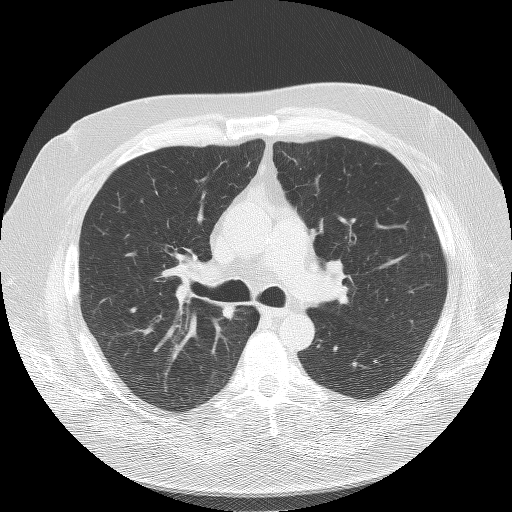
Axial slice from a low-dose chest CT screening exam; third screening round (two years after baseline); lung window (W 1500 / L -600 HU); 2.5 mm slice thickness; lung (sharp) reconstruction kernel (BONE); slice 46 of 136 in the series. Male participant, aged 58 years at enrolment. Former smoker at enrolment.
• Lesion marked by an expert reader, bounding box (x1, y1, x2, y2) in pixels: (198, 288, 255, 338).
• The exam's reader record, not a measurement of the box and not confirmed to be the same lesion: non-calcified nodule or mass ≥4 mm, right upper lobe, 9 × 8 mm, spiculated (stellate) margins, soft tissue attenuation, pre-existing on the prior screen: yes; interval growth: yes.
• Lung cancer was diagnosed 157 days after this screen: squamous cell carcinoma, NOS, right upper lobe, moderately differentiated (G2), stage IA (AJCC 6th edition), 18 mm at pathology.